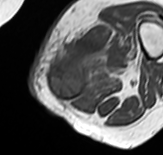
MRI of an extremity soft-tissue mass, one axial slice; position 18 of 65 along the scan axis; MR volume resampled by the dataset authors to the PET/CT grid (not the native acquisition matrix); 163 × 155 image matrix, field of view 159 × 151 mm. Female patient. Case-level facts recorded for this patient, not image findings: histological type: pleomorphic leiomyosarcoma; grade: high; site of the primary tumour: left thigh.
Annotated regions visible in this slice (expert contour drawn on MRI and transferred to this co-registered scan by the dataset authors):
- gross tumour volume including surrounding oedema: bounding box (x1, y1, x2, y2) in pixels: (48, 26, 136, 102)
- gross tumour volume (mass): (48, 56, 90, 100)